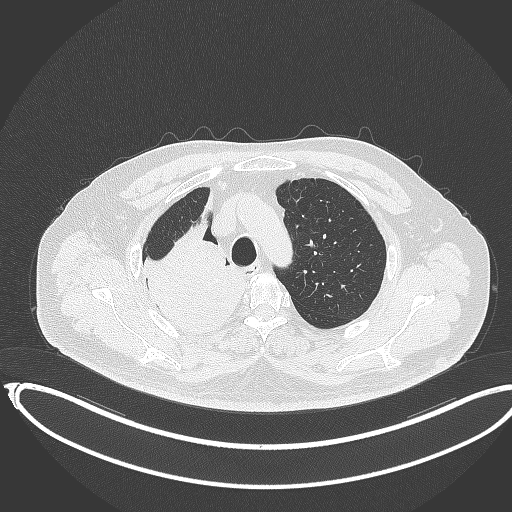
Chest CT, one axial slice; position 288 of 403 along the scan axis; reconstruction kernel B70f; 120 kVp; lung window (W 1500 / L -600 HU); 1 mm slice thickness; 512 × 512 image matrix, field of view 436 × 436 mm. Patient: male, 68 years. From the clinical record (not read from this slice): clinical TNM (as recorded): T2a N0 M0.
Structures marked on this image (bounding box drawn by a radiologist):
- lung tumour (recorded histology: adenocarcinoma): bounding box [x1, y1, x2, y2] px = [138, 209, 253, 342]